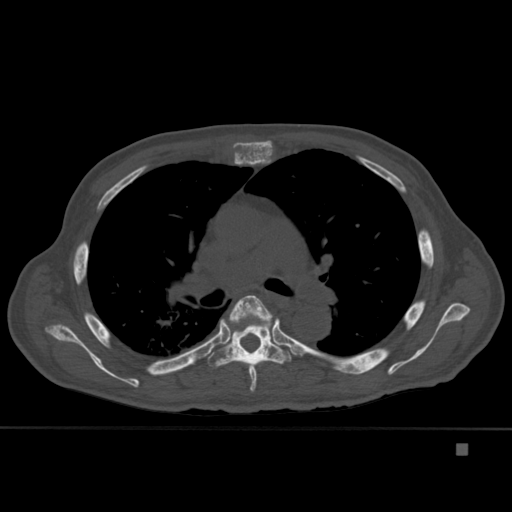
CT including the spine, one axial slice; bone window (W 1800 / L 400 HU); 1.5 mm slice thickness; 512 × 512 image matrix, field of view 378 × 378 mm. Male patient, age 75 years. Case-level facts recorded for this patient, not image findings: primary cancer: prostate.
Annotated regions visible in this slice (semi-automatically segmented with operator editing):
- T5 vertebra: bounding box <219,295,280,392> (left, top, right, bottom; pixels)
- T6 vertebra: <208,315,292,368>